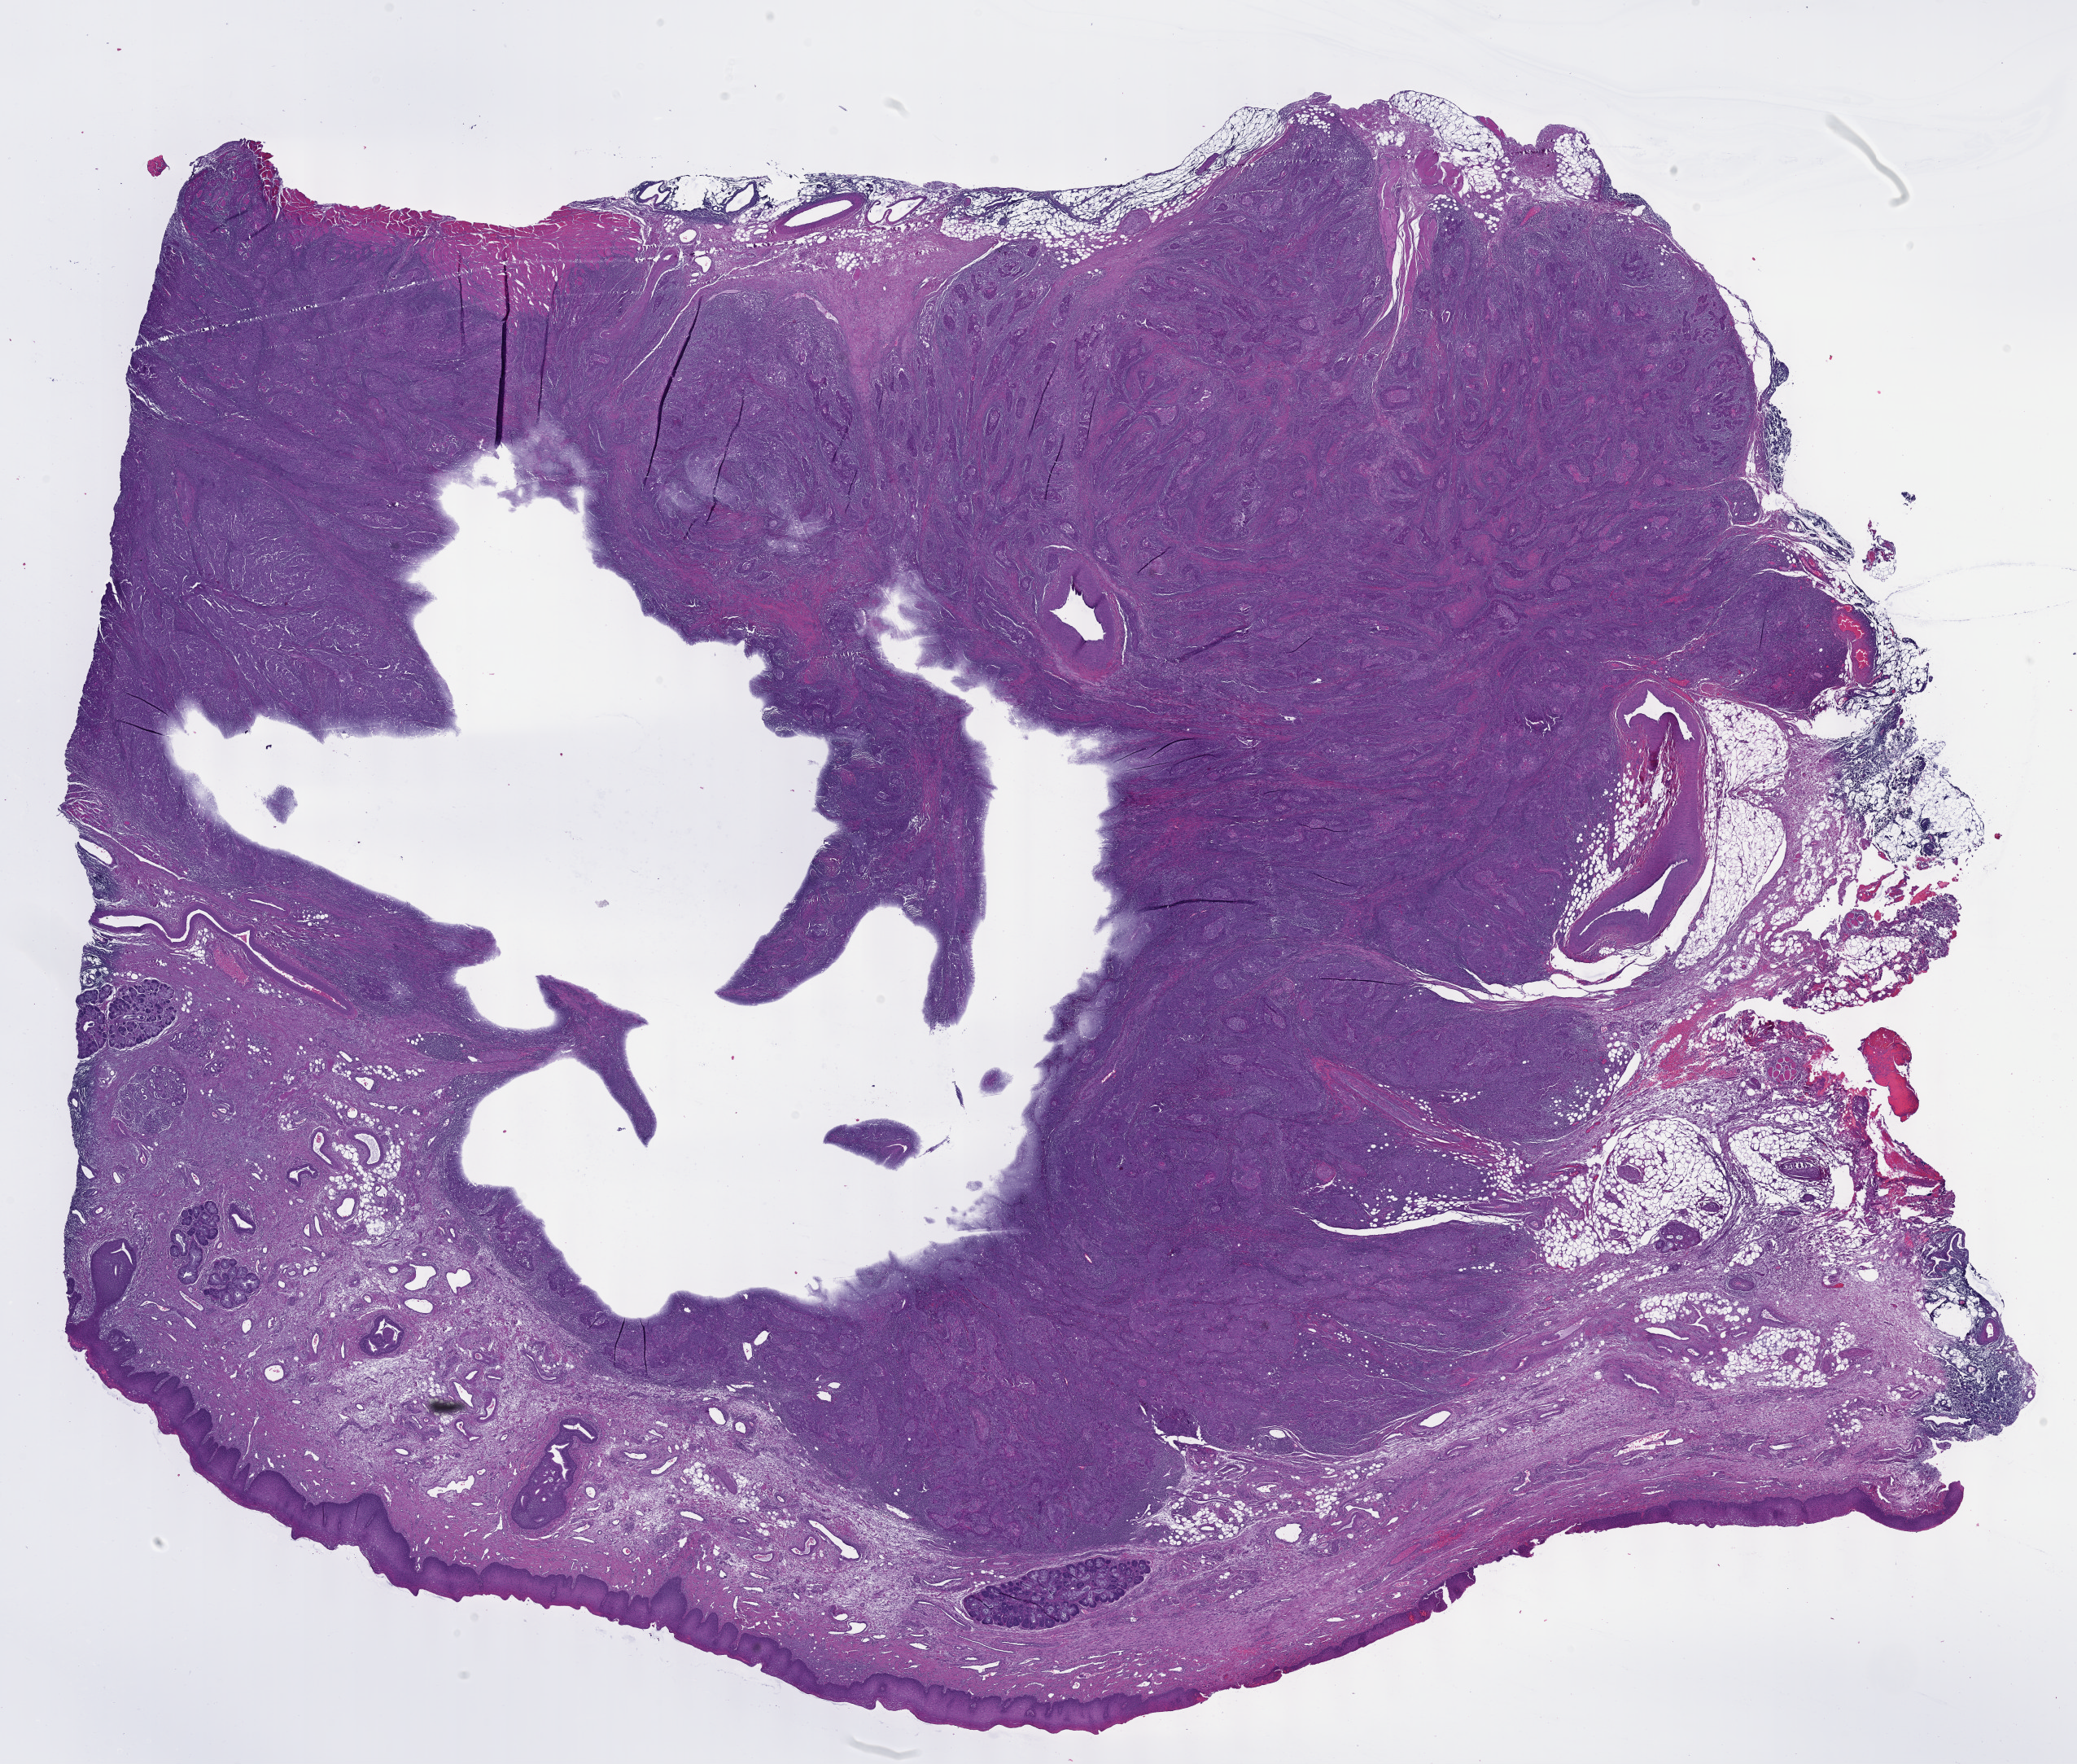
H&E-stained whole-slide image — a low-resolution overview of the entire scanned area, about 20.6 x 17.5 mm, formalin-fixed paraffin-embedded (FFPE) diagnostic section, head and neck, primary tumour sample. Patient: male, age at initial diagnosis 75 years. Histologic grade: G3 (poorly differentiated).
- histologic diagnosis: Squamous cell carcinoma, NOS (larynx, NOS)